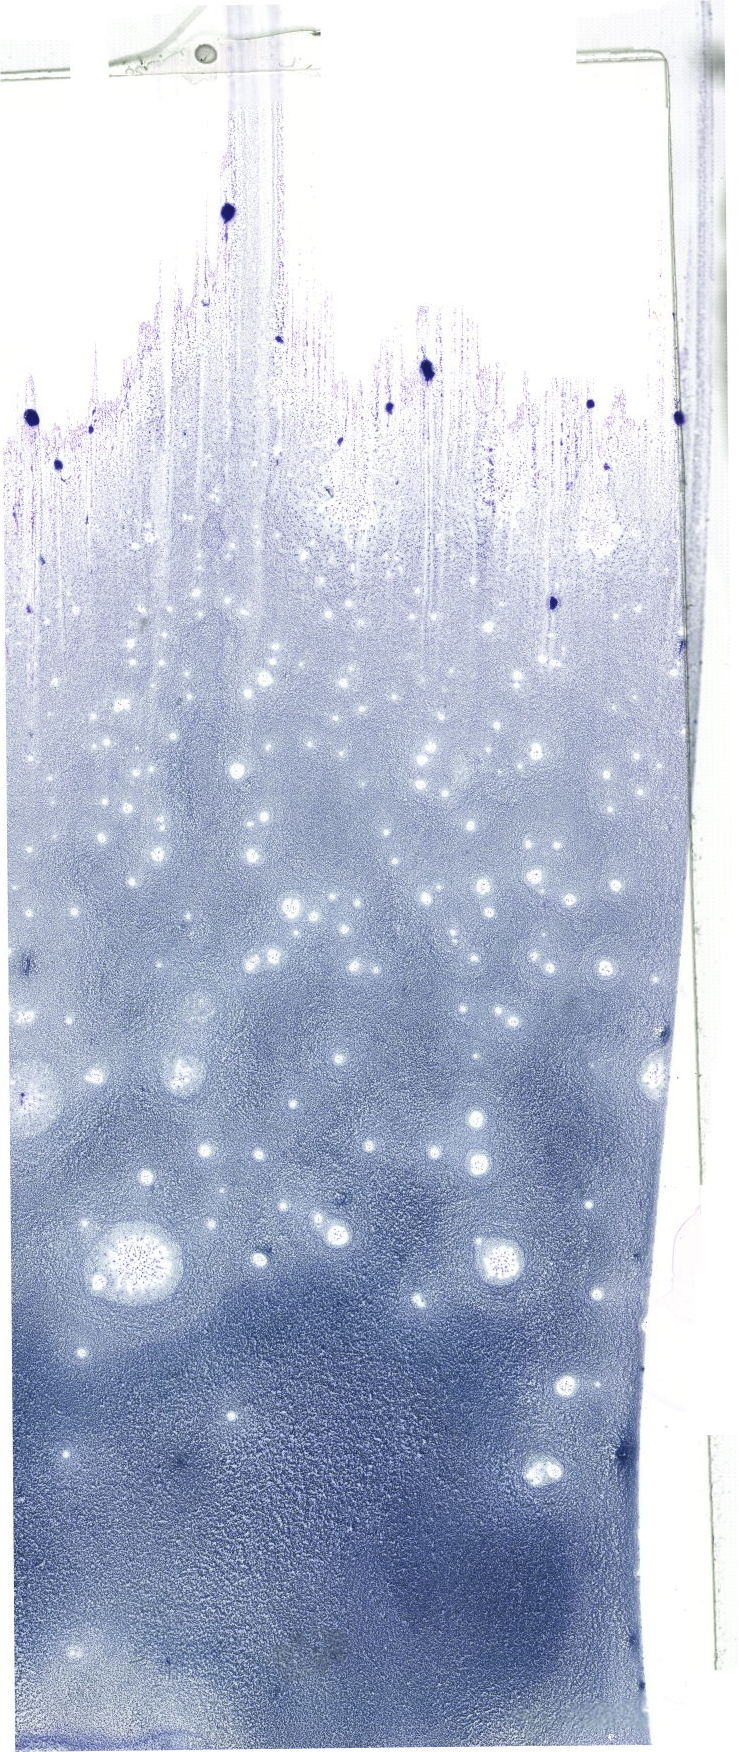
Bone marrow aspirate smear, May-Grünwald–Giemsa stain, whole-slide image, whole scanned area (about 20.9 x 49.7 mm) shown as a low-resolution overview. Female patient.
* diagnosis: B Acute Lymphoblastic Leukemia